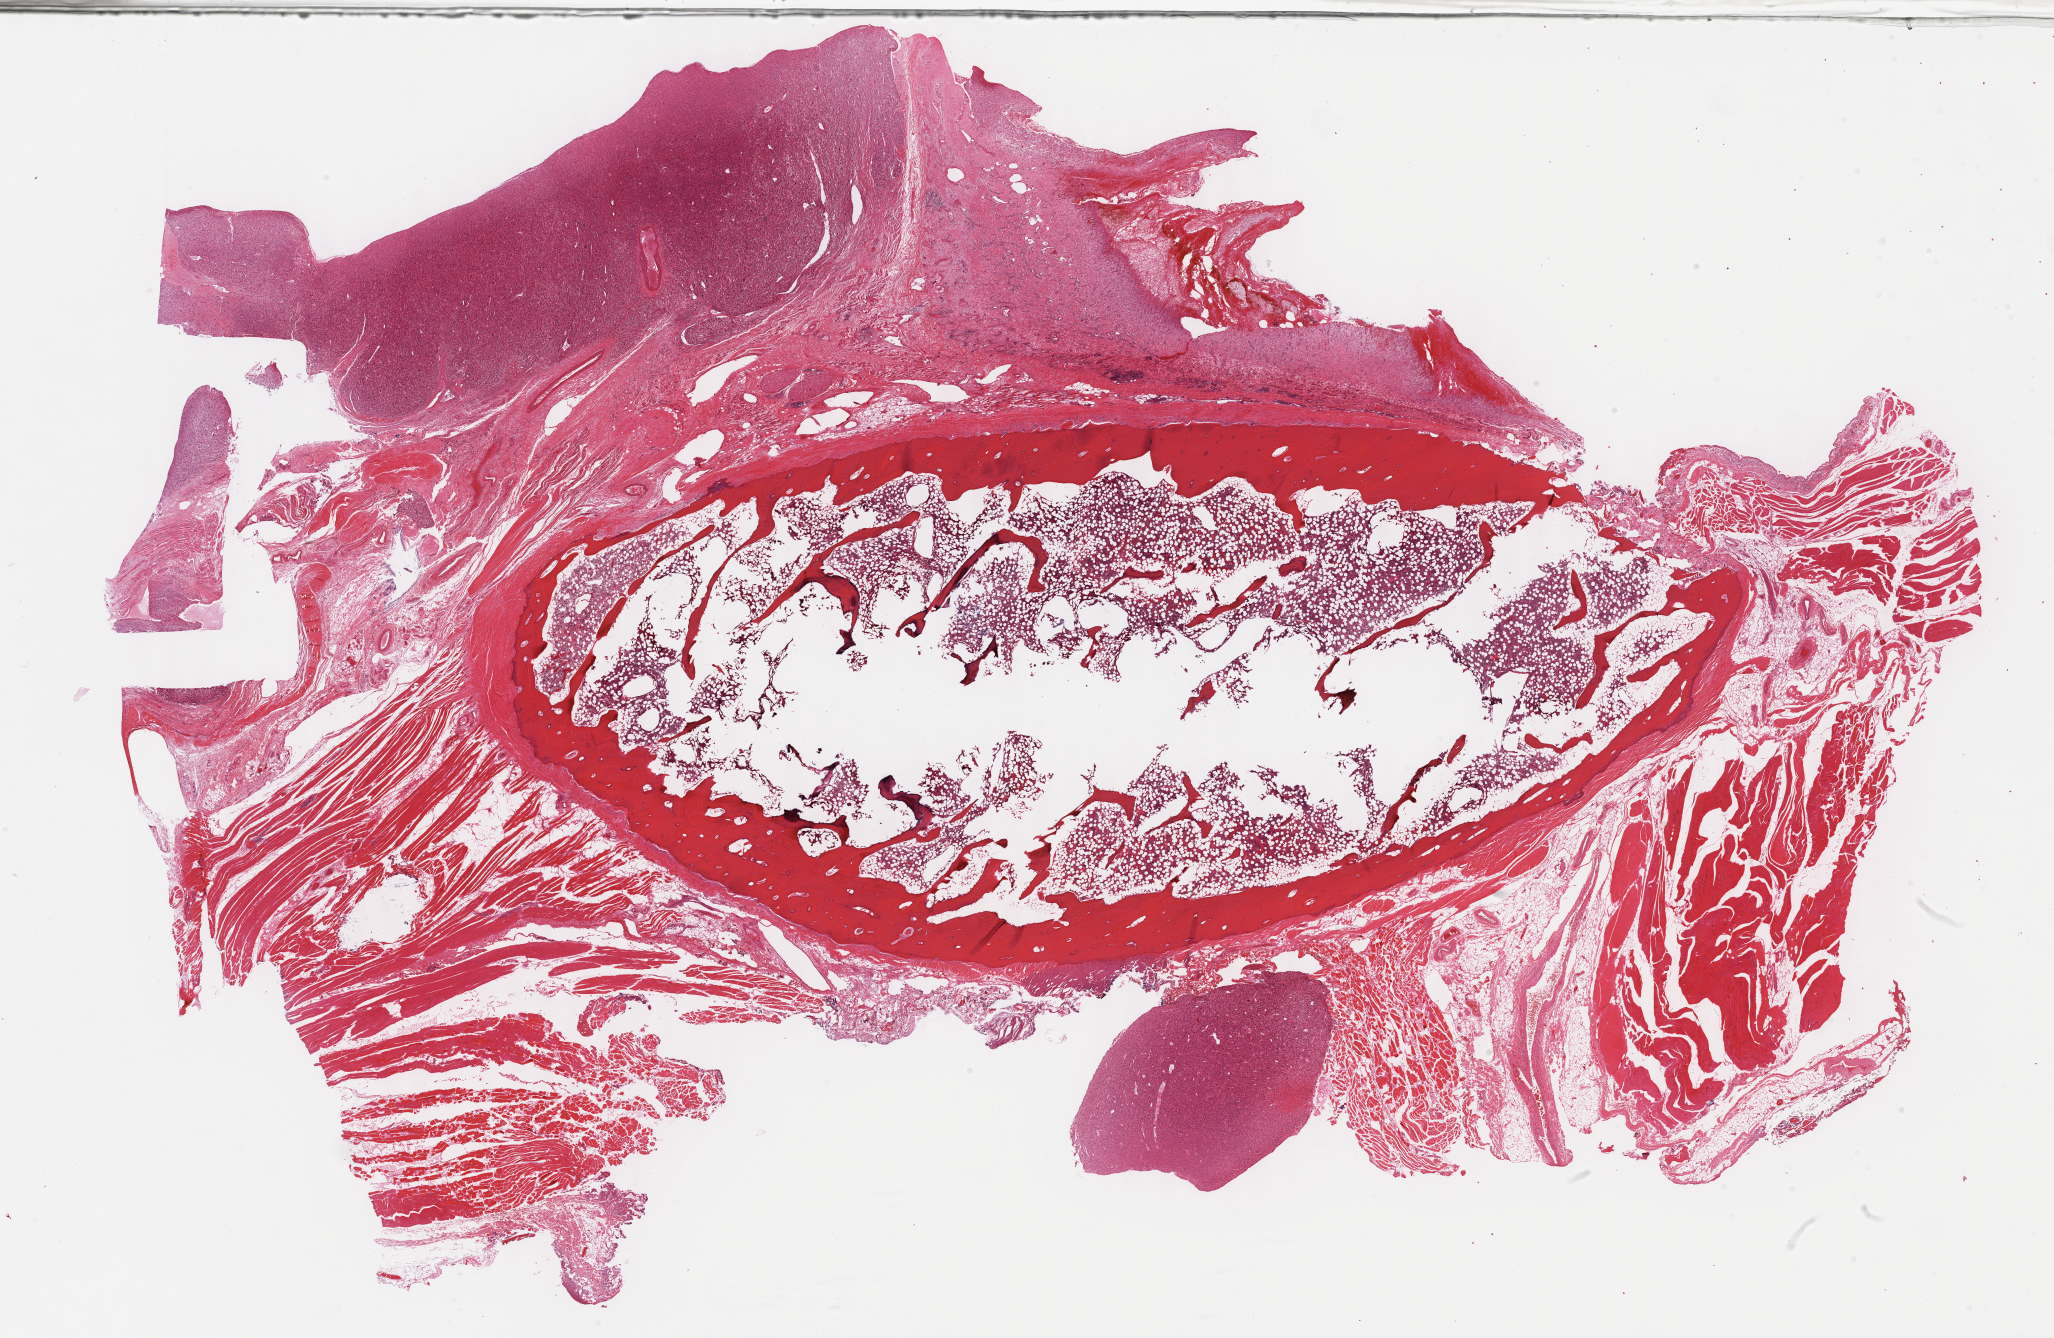
Hematoxylin and eosin (H&E) stained whole-slide image, low-resolution overview of the scanned area, about 33.2 x 21.6 mm (slide scanned at 40x); formalin-fixed paraffin-embedded (FFPE) diagnostic section; sample: primary tumour, connective, subcutaneous and other soft tissues. Patient: female, age at initial diagnosis 49 years.
Histologic diagnosis: Undifferentiated sarcoma (connective, subcutaneous and other soft tissues of thorax).